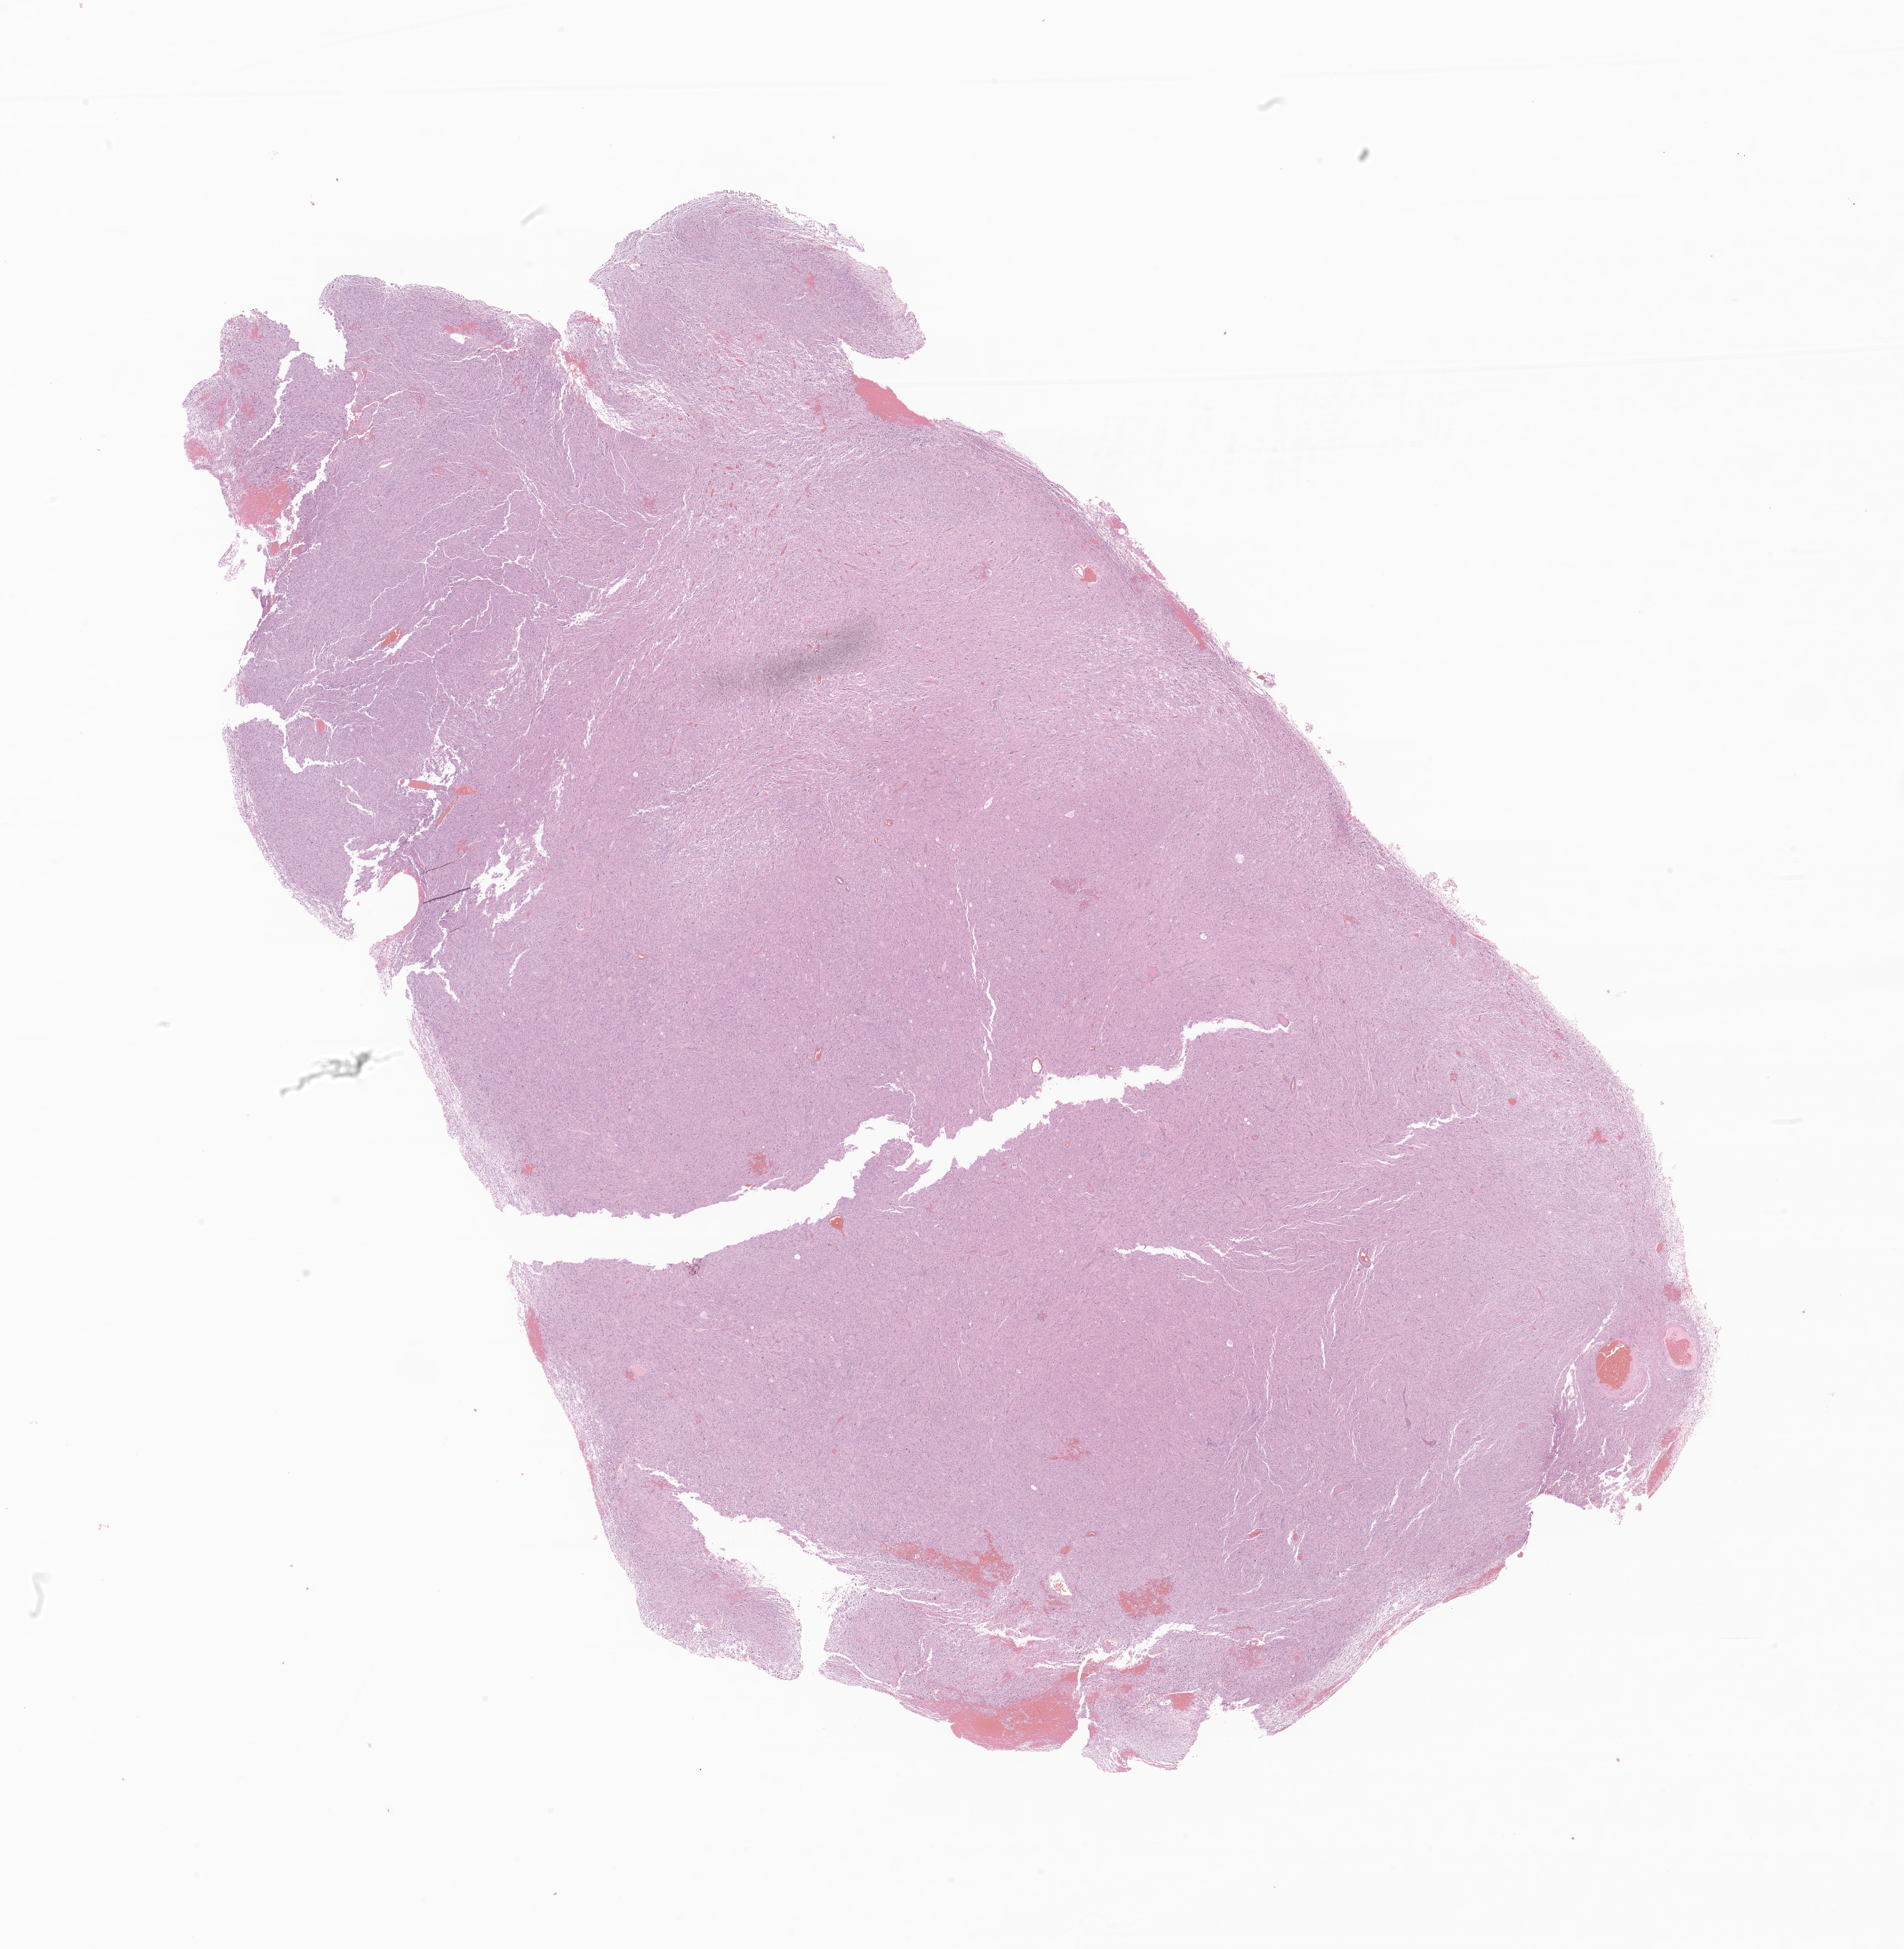
Digitized haematoxylin and eosin-stained section of tumor tissue from the temporal lobe — shown as a low-resolution overview of the whole scanned area (about 20.1 x 20.6 mm); formalin-fixed, paraffin-embedded (FFPE) tissue. Patient: male, age 225 months.
Recorded diagnosis: Pleomorphic xanthoastrocytoma, NOS.